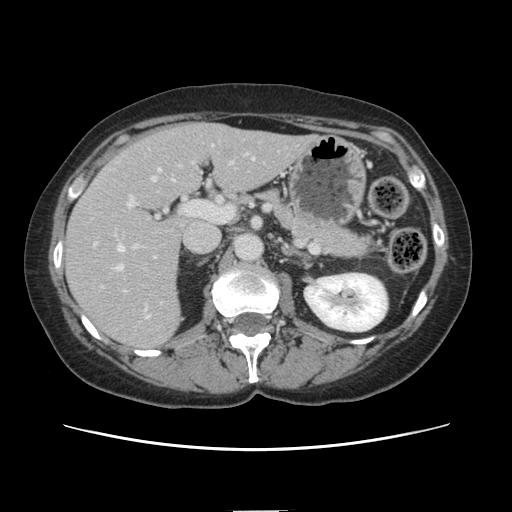
Contrast-enhanced abdominal CT, one axial slice; position 73 of 141 along the scan axis; intravenous contrast given; soft-tissue window (W 400 / L 40 HU); 2.5 mm slice thickness; 512 × 512 image matrix. Female patient, age 63 years. From the clinical record (not read from this slice): diagnosis: colorectal cancer liver metastases, imaged before liver resection; multiple liver metastases: yes; largest metastasis: 3.2 cm.
Outlined on this slice (manually delineated by an expert):
- hepatic veins: bounding box [x1, y1, x2, y2] px = [114, 169, 160, 272]
- liver: [67, 125, 309, 350]
- planned liver remnant (the part of the liver to remain after resection): [175, 124, 310, 193]
- portal vein (with intrahepatic branches): [117, 195, 150, 318]